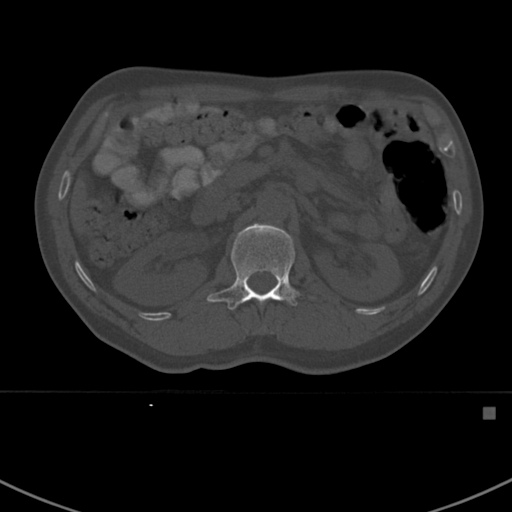
CT including the spine, one axial slice; slice 309 of 412 in the series (ordered by position); reconstruction kernel Br40s; 120 kVp; bone window (W 1800 / L 400 HU); 1.5 mm slice thickness; 512 × 512 image matrix, field of view 358 × 358 mm. Patient: male, 59 years. Case-level facts recorded for this patient, not image findings: primary cancer: prostate.
Outlined on this slice (semi-automatically segmented with operator editing):
- L1 vertebra: bounding box <207,224,313,310> (left, top, right, bottom; pixels)